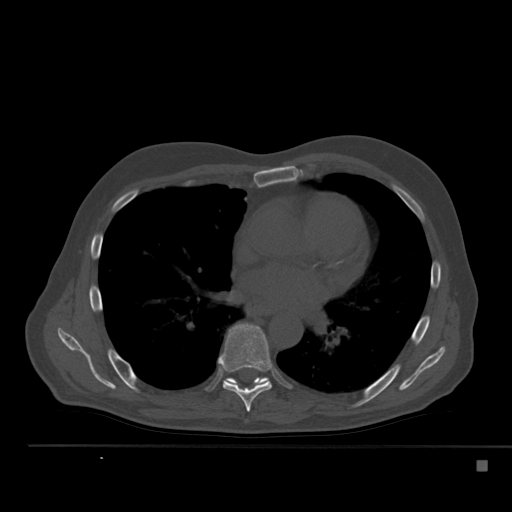
CT including the spine, one axial slice; position 323 of 517 along the scan axis; reconstruction kernel Br40s; 120 kVp; bone window (W 1800 / L 400 HU); 512 × 512 image matrix, field of view 408 × 408 mm. Male patient, age 70 years. Case-level facts recorded for this patient, not image findings: primary cancer: renal; vertebrae with lytic lesions (as recorded): T4, T6, T10, T12, L3, L4, L5.
Outlined on this slice (semi-automatically segmented with operator editing):
- T7 vertebra: bounding box [x1, y1, x2, y2] px = [219, 323, 272, 412]
- T8 vertebra: [227, 377, 269, 382]